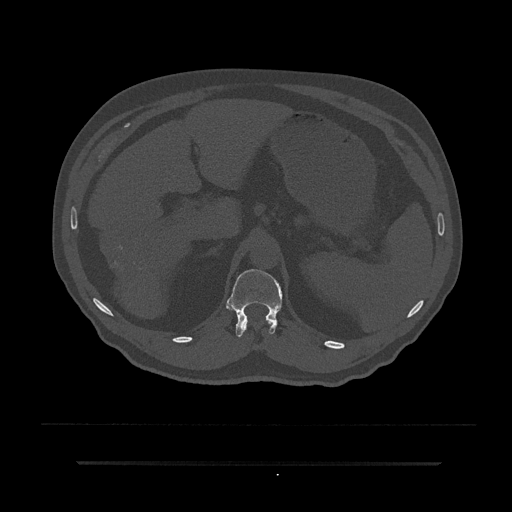
CT including the spine, one axial slice. Slice 228 of 797 in the series (ordered by position). Reconstruction kernel Br40s/3. 120 kVp. Bone window (W 1800 / L 400 HU). 0.5 mm slice thickness. 512 × 512 image matrix, field of view 464 × 464 mm. Patient: male, 59 years. From the clinical record (not read from this slice): primary cancer: bile ducts; vertebrae with lytic lesions (as recorded): T10.
Outlined on this slice (semi-automatically segmented with operator editing):
- T11 vertebra: bounding box (x1, y1, x2, y2) in pixels: (244, 322, 271, 329)
- T12 vertebra: (227, 269, 283, 337)